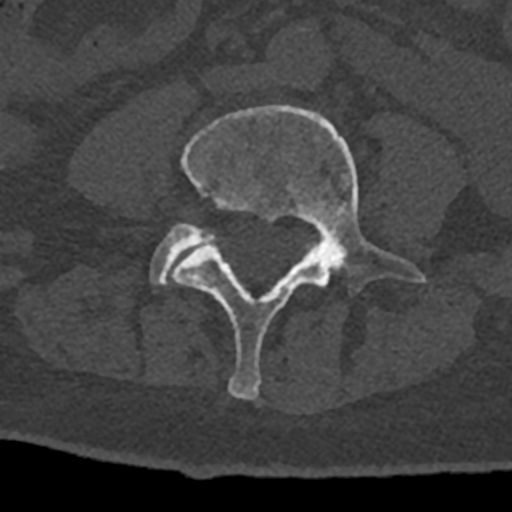
CT including the spine, one axial slice. Slice 249 of 797 in the series (ordered by position). 120 kVp. Bone window (W 1800 / L 400 HU). 0.5 mm slice thickness. 512 × 512 image matrix, field of view 160 × 160 mm. Male patient, age 74 years. From the clinical record (not read from this slice): primary cancer: renal.
Structures marked on this image (semi-automatic segmentation, software-assisted and operator-edited):
- L4 vertebra: bounding box [x1, y1, x2, y2] px = [172, 105, 426, 400]
- L5 vertebra: [150, 223, 215, 285]